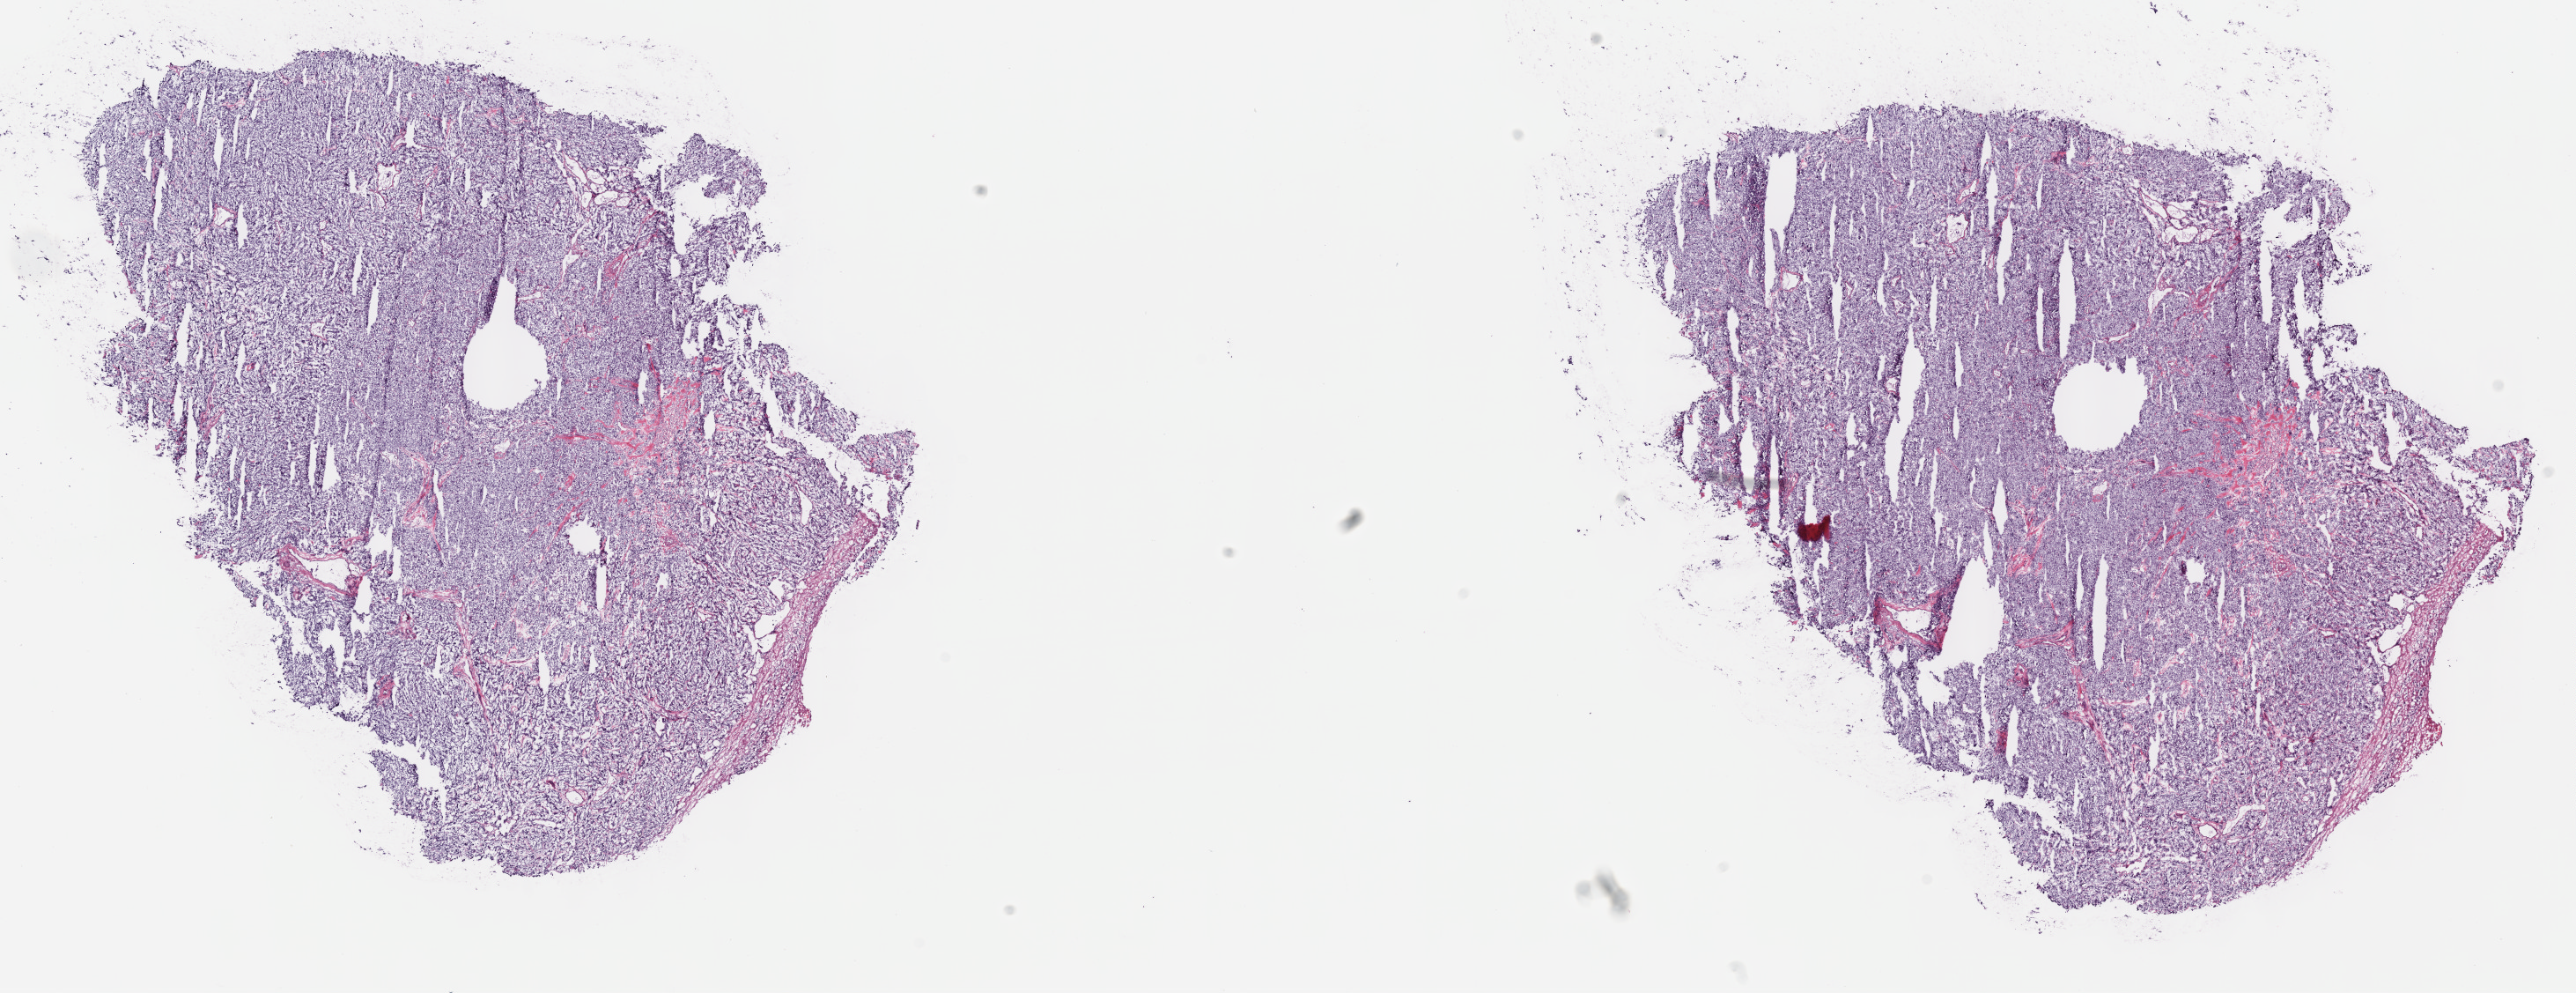
Digitized H&E tissue section (whole slide), whole scanned area (about 23.7 x 9.1 mm, from a 40x scan) shown as a low-resolution overview, frozen section from the top of the tissue portion, adrenal gland, primary tumour sample. Male patient; age at initial diagnosis 37 years. Pathologist review of this section (percent, as recorded): tumour cells 80%, tumour nuclei 80%, normal cells 0%, stromal cells 20%, necrosis 0%. Inflammatory infiltration, as recorded: lymphocyte infiltration 0%, monocyte infiltration 0%, neutrophil infiltration 0%.
- laterality: left
- diagnosis: Pheochromocytoma, NOS